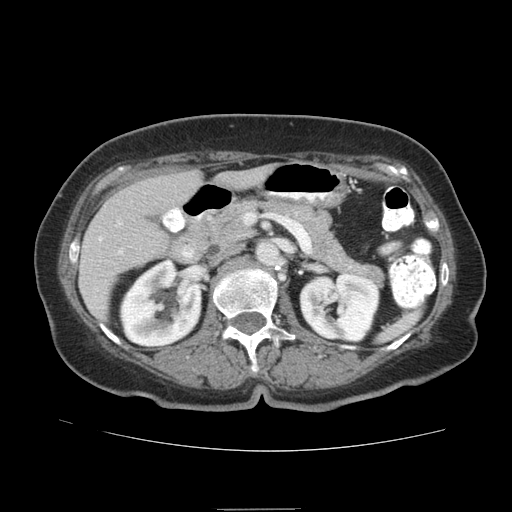
Contrast-enhanced abdominal CT (liver protocol), one axial slice; position 35 of 95 along the scan axis; soft-tissue window (W 400 / L 40 HU); 2.5 mm slice thickness; 512 × 512 image matrix, field of view 360 × 360 mm. Case-level facts recorded for this patient, not image findings: diagnosis: hepatocellular carcinoma (patient treated with transarterial chemoembolisation; whether this scan precedes or follows treatment is not stated here); TNM stage (as recorded): Stage-IVA; Child-Pugh class: B; tumour nodularity: uninodular.
Annotated regions visible in this slice (semi-automatically segmented with operator editing):
- liver parenchyma outside the tumour (the mass and vessels are separate outlines, so this box may not span the whole liver): box from (x=82, y=164) to (x=274, y=278) px
- liver vessels: (x=99, y=238)–(x=122, y=253)